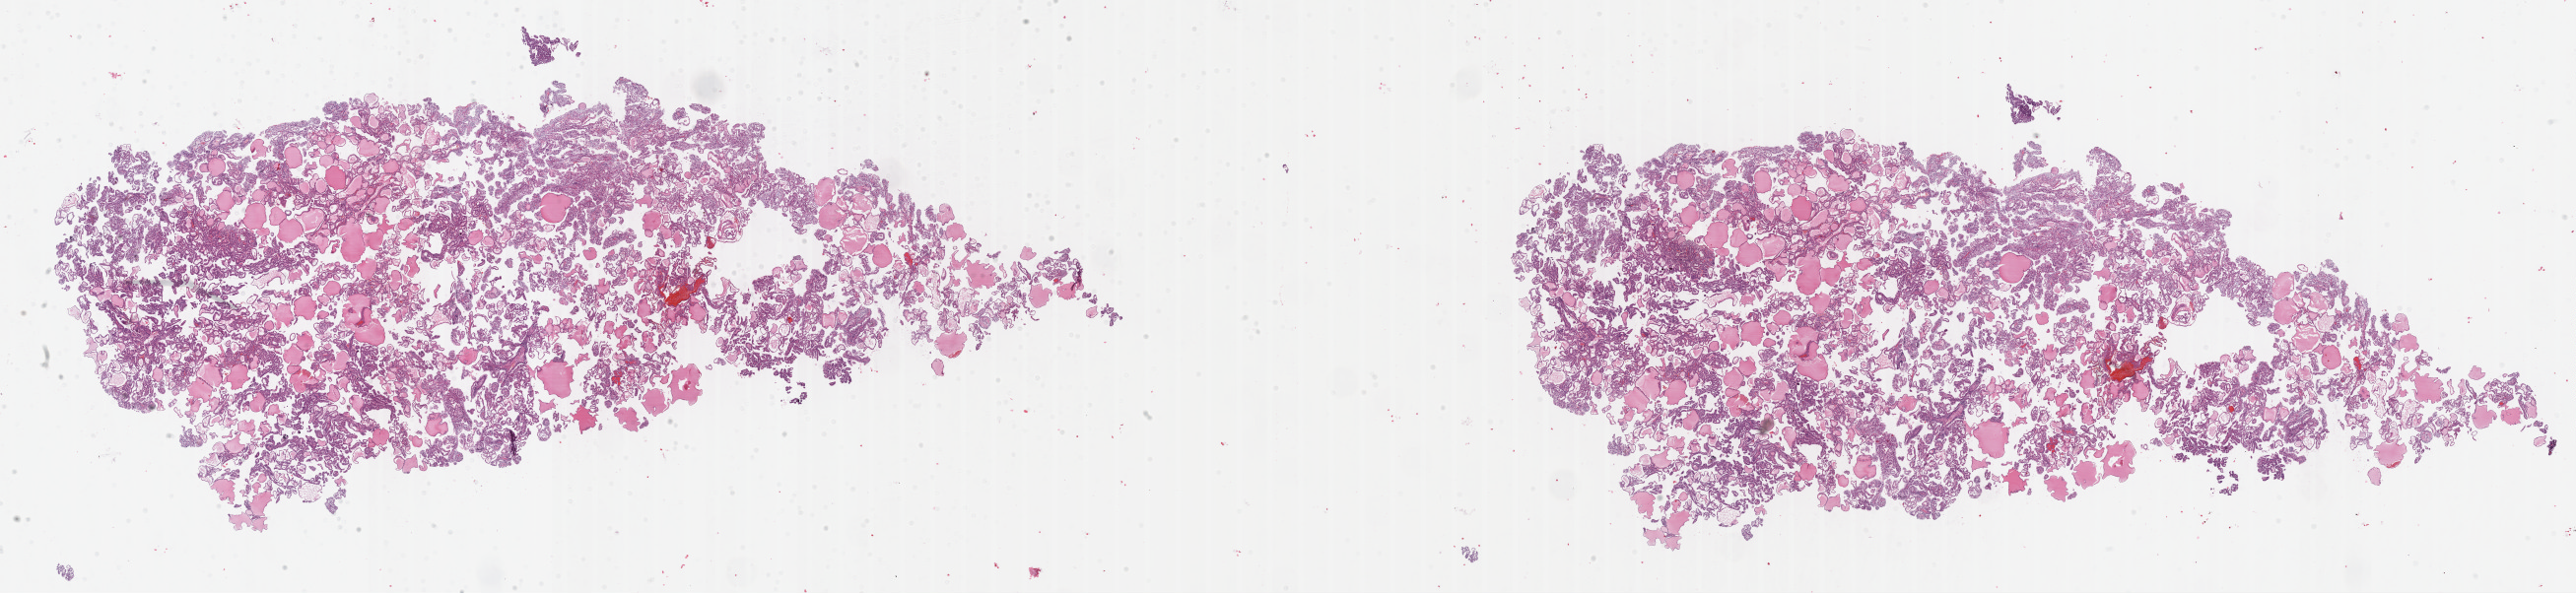
H&E-stained whole-slide image, whole scanned area (about 42.3 x 9.7 mm, from a 40x scan) shown as a low-resolution overview, FFPE section, primary tumour sample from the kidney. Female, age 66 years at initial diagnosis.
Lymph nodes positive (case pathology): 0 of 16 examined. Diagnosis: Papillary adenocarcinoma, NOS. TNM: T1b N0 MX. AJCC pathologic stage: I.